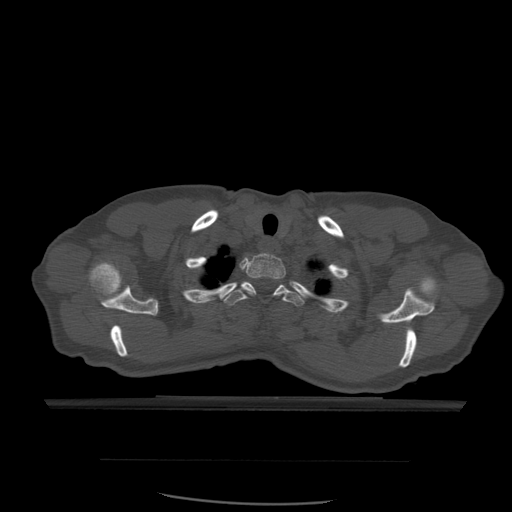
CT including the spine, one axial slice; slice 463 of 574 in the series (ordered by position); bone window (W 1800 / L 400 HU); 1.25 mm slice thickness; 512 × 512 image matrix, field of view 392 × 392 mm. Patient age 48 years. From the clinical record (not read from this slice): primary cancer: lung.
Annotated regions visible in this slice (semi-automatically segmented with operator editing):
- T1 vertebra: box from (x=245, y=253) to (x=286, y=300) px
- T2 vertebra: (x=224, y=281)–(x=305, y=306)